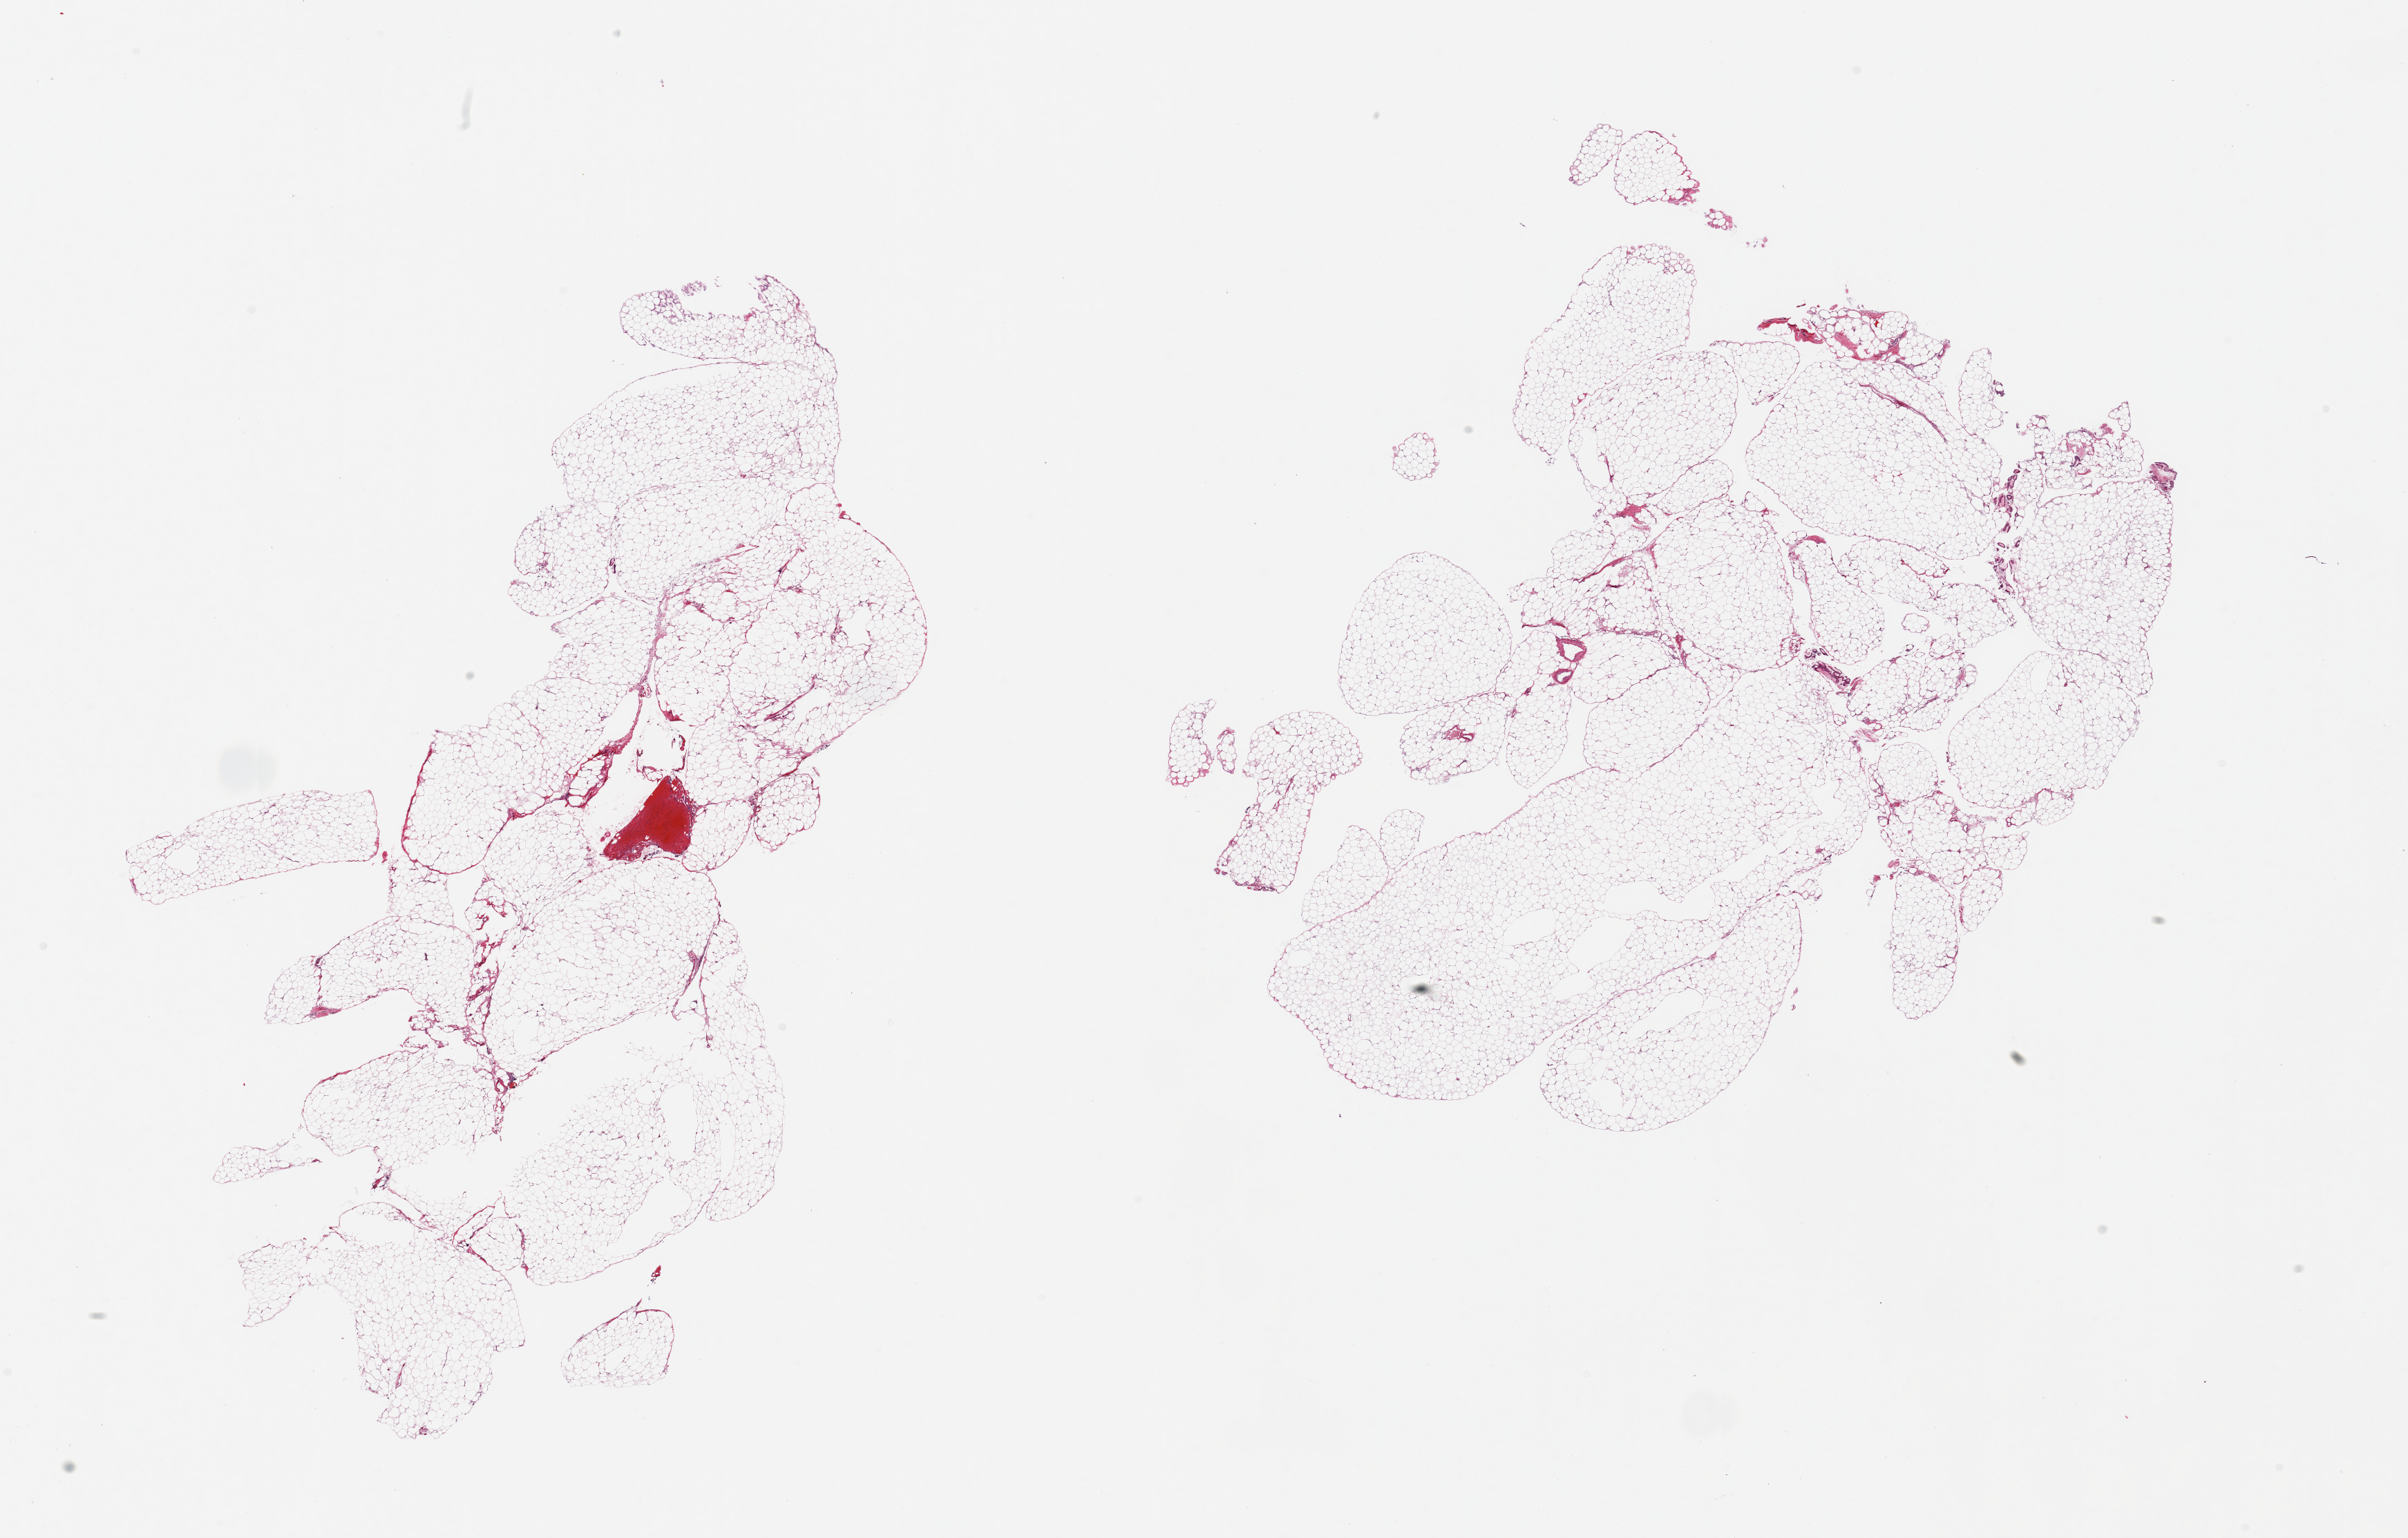
Digitized haematoxylin and eosin-stained section, shown as a low-resolution overview of the whole scanned area (about 27.6 x 17.6 mm, slide scanned at 20x); PAXgene-fixed, paraffin-embedded tissue; target tissue: omentum; donor tissue sample. Donor sex: male.
Pathologist's review note for this sample: 2 pieces; mature adipose tissue, several detached fragments of glands/carryover.